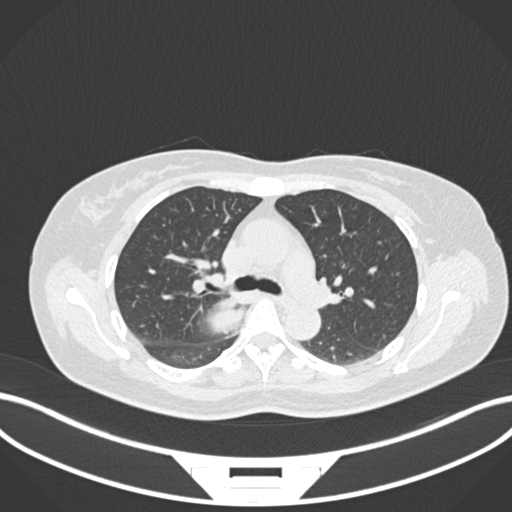
Chest CT, one axial slice; position 623 of 677 along the scan axis; reconstruction kernel B30f; 120 kVp; lung window (W 1500 / L -600 HU); 1 mm slice thickness; 512 × 512 image matrix, field of view 400 × 400 mm. Patient: female, 54 years. Case-level facts recorded for this patient, not image findings: clinical TNM (as recorded): T4 N0 M0.
Outlined on this slice (bounding box drawn by a radiologist):
- lung tumour (recorded histology: adenocarcinoma): bounding box (x1, y1, x2, y2) in pixels: (200, 296, 249, 333)